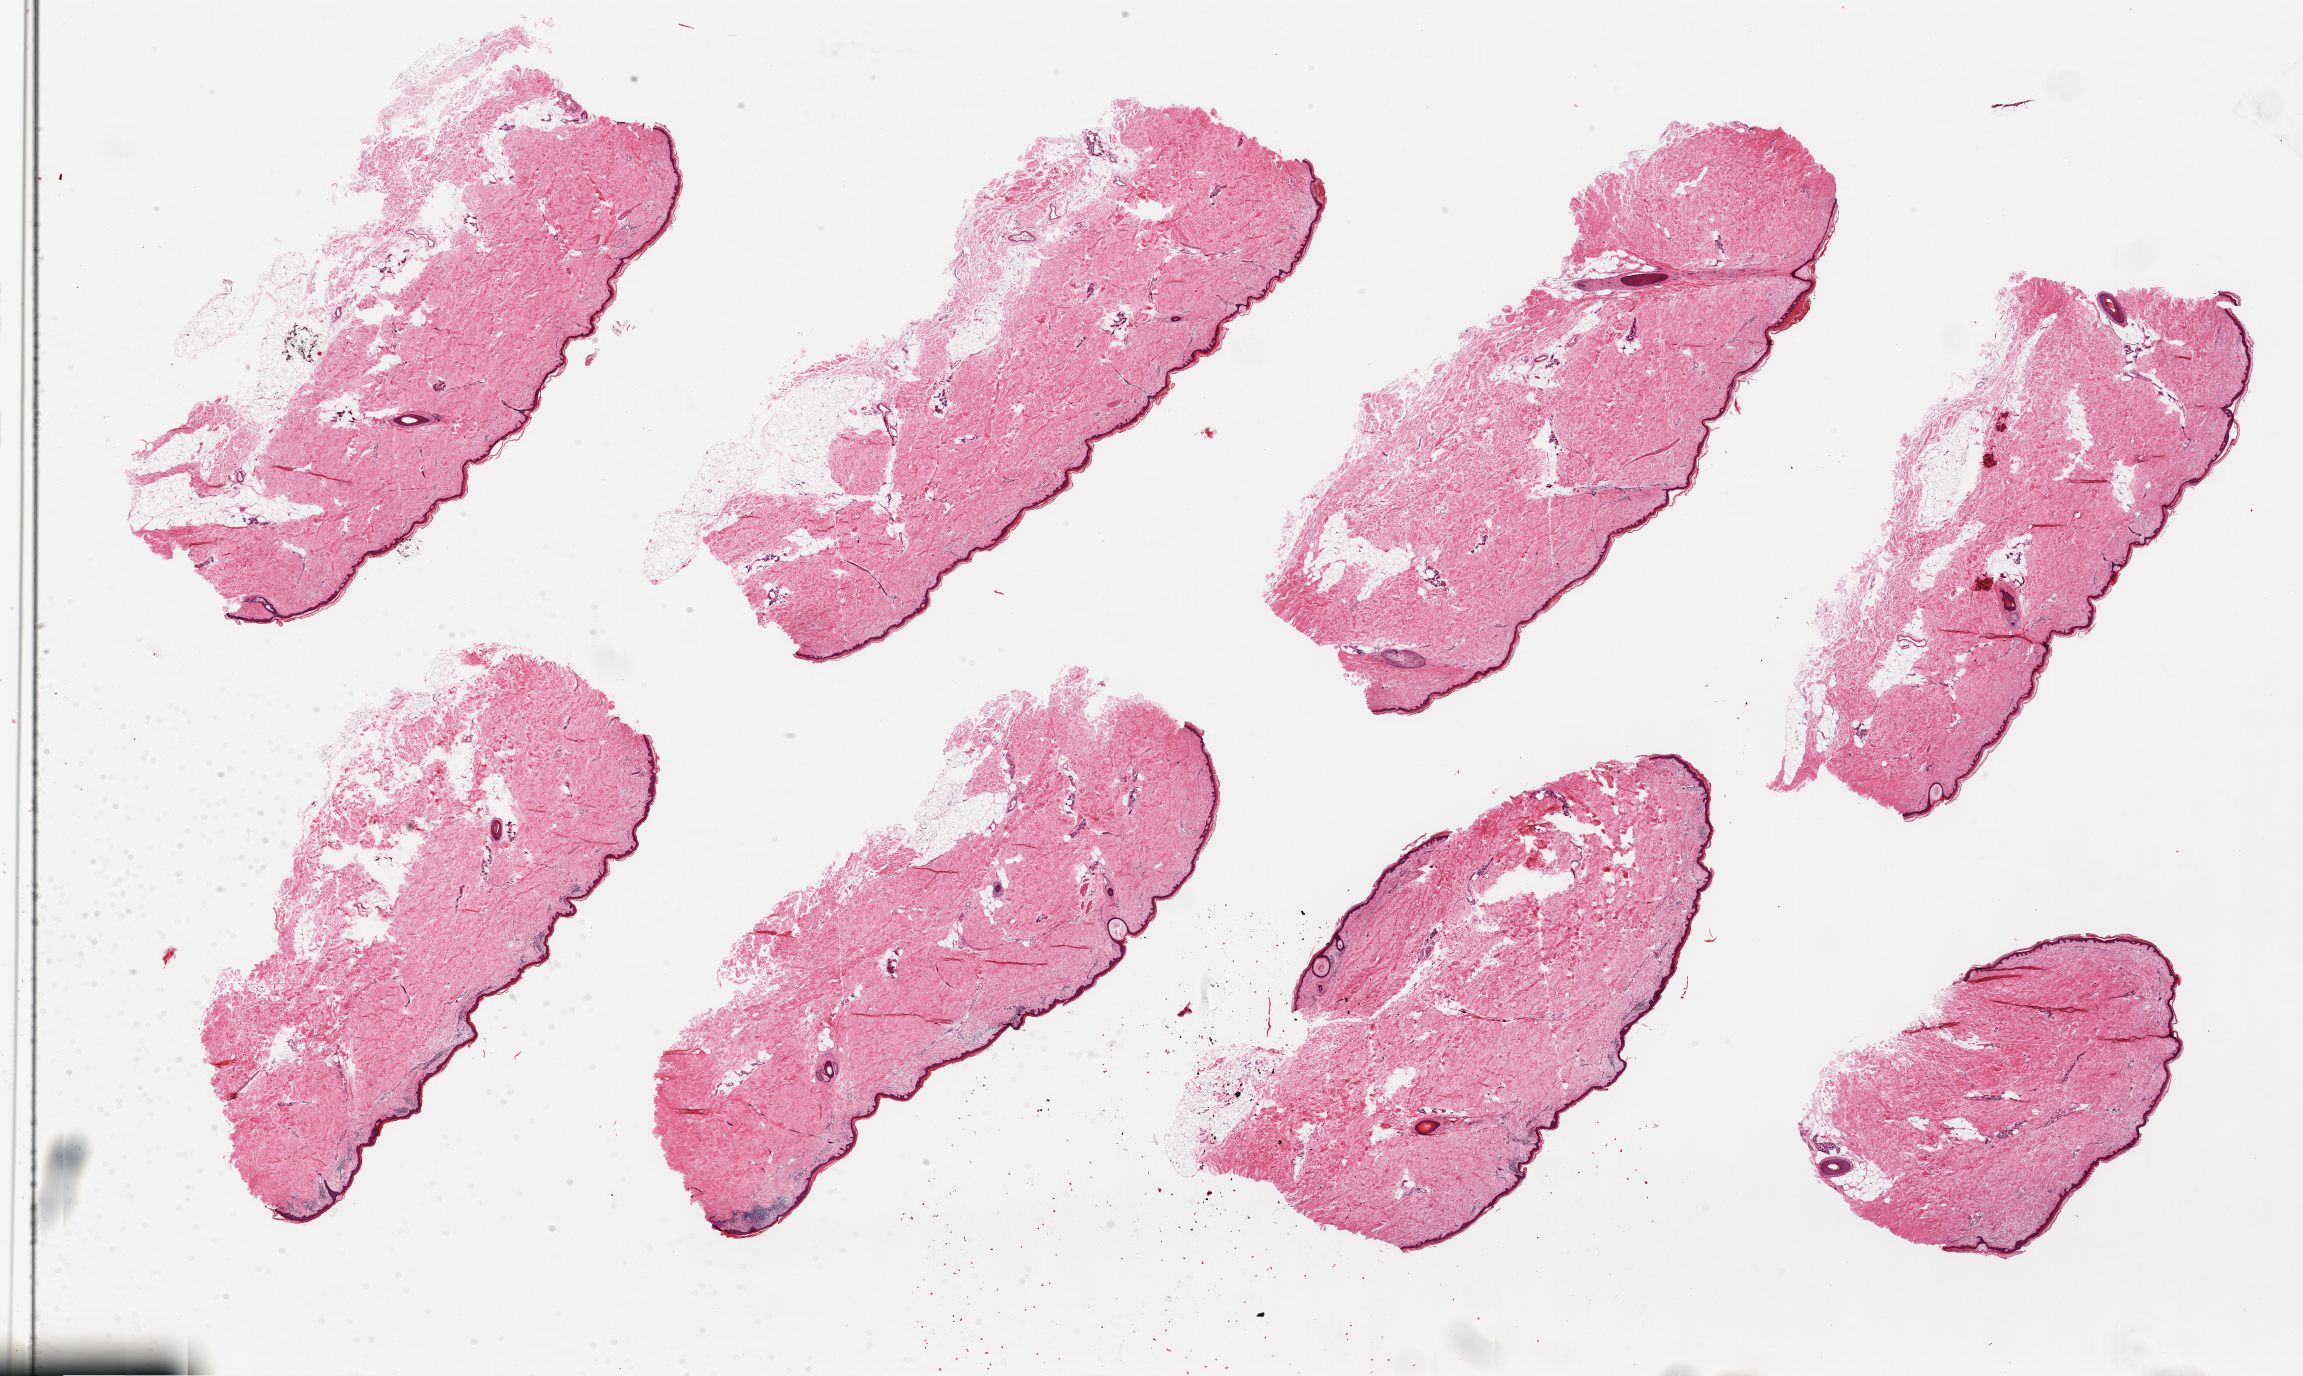
Whole-slide image, haematoxylin and eosin stain, brightfield, whole scanned area (about 36.4 x 21.8 mm) shown as a low-resolution overview, PAXgene-fixed paraffin-embedded (PFPE) section, target tissue: skin of lower leg, donor tissue sample.
Review note (as recorded): 8 pieces ~10x4mm. Squamous mucosa is 1-2% thickness.